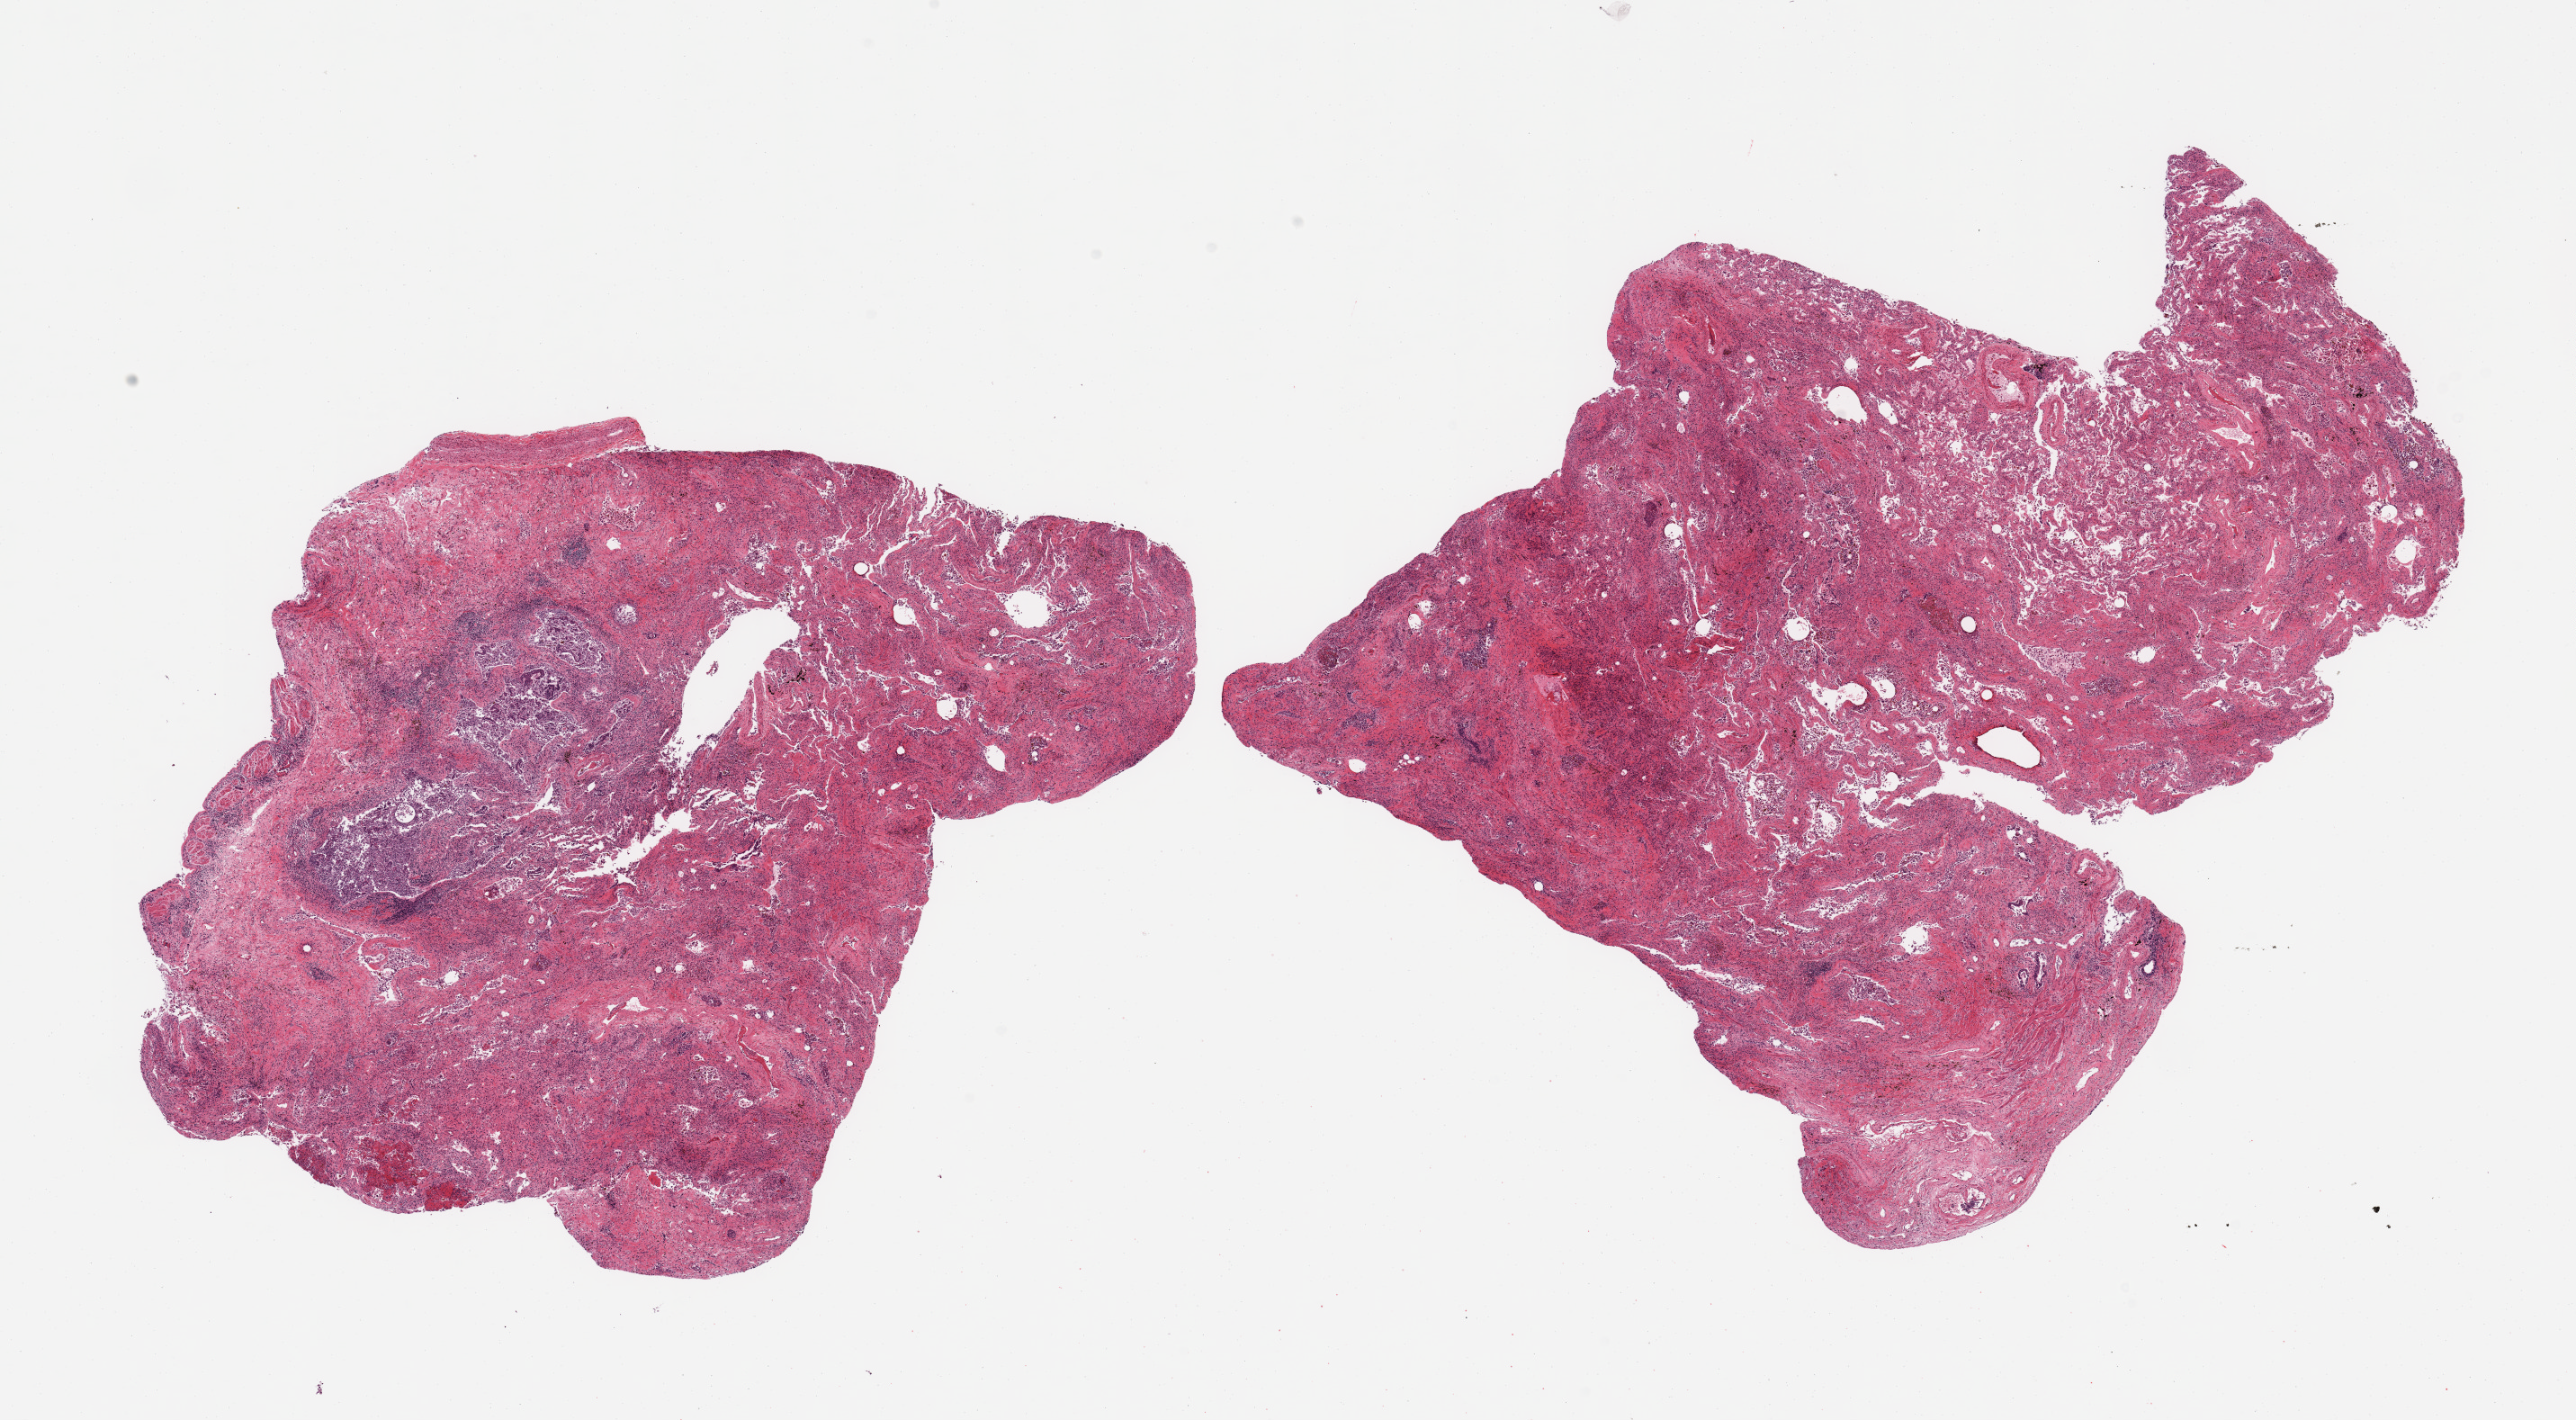
Whole-slide image, haematoxylin and eosin stain, a low-resolution overview of the entire scanned area, about 22.6 x 12.5 mm. PAXgene-fixed, paraffin-embedded tissue. Target tissue: lung. Tissue donor sample. Donor sex: female.
Reviewer comment on this tissue sample: 2 pieces; extensive fibrosis and bronchiectasis; no normal lung.